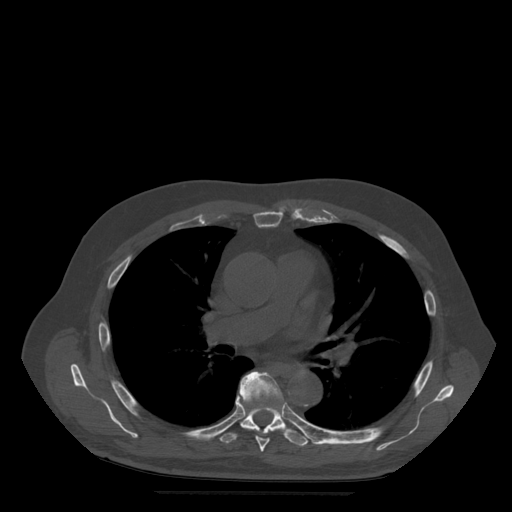
CT including the spine, one axial slice; position 343 of 522 along the scan axis; bone window (W 1800 / L 400 HU); 512 × 512 image matrix, field of view 420 × 420 mm. Patient age 72 years. Case-level facts recorded for this patient, not image findings: primary cancer: prostate.
Outlined on this slice (semi-automatically segmented with operator editing):
- T6 vertebra: bounding box [x1, y1, x2, y2] px = [238, 372, 283, 452]
- T7 vertebra: [219, 390, 309, 447]